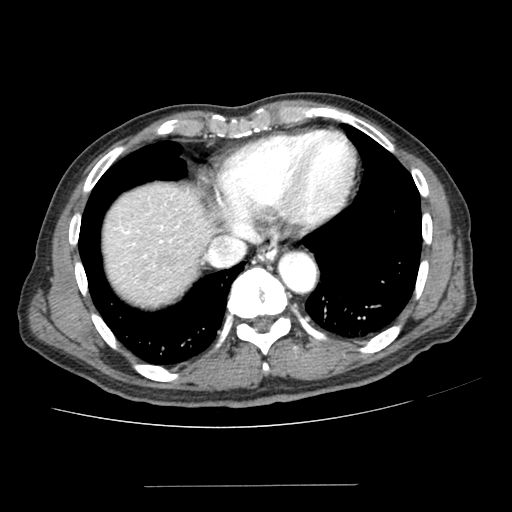
Contrast-enhanced abdominal CT (liver protocol), one axial slice; slice 177 of 187 in the series (ordered by position); 100 kVp; one of 2 acquisitions stored at this slice position; soft-tissue window (W 400 / L 40 HU); 2.5 mm slice thickness; 512 × 512 image matrix, field of view 360 × 360 mm. From the clinical record (not read from this slice): diagnosis: hepatocellular carcinoma (patient treated with transarterial chemoembolisation; whether this scan precedes or follows treatment is not stated here); TNM stage (as recorded): Stage-I; Child-Pugh class: A; tumour differentiation: poorly differentiated.
Outlined on this slice (semi-automatic segmentation, software-assisted and operator-edited):
- abdominal aorta: box from (x=278, y=251) to (x=316, y=291) px
- liver parenchyma outside the tumour (the mass and vessels are separate outlines, so this box may not span the whole liver): (x=104, y=184)–(x=214, y=306)
- mass: (x=141, y=244)–(x=182, y=281)
- liver vessels: (x=115, y=225)–(x=179, y=289)